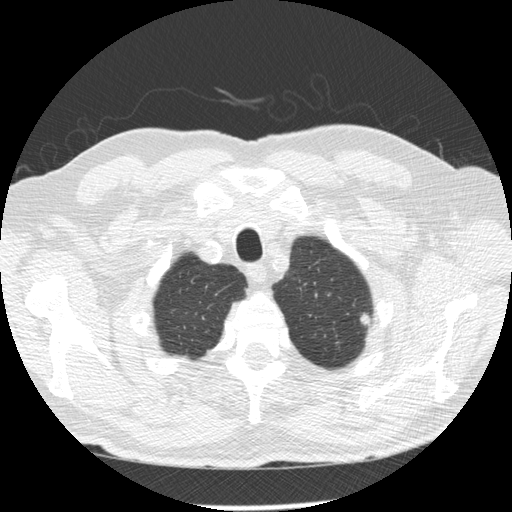
Axial slice from a low-dose chest CT screening exam; third annual screen; lung window (W 1500 / L -600 HU); 2.5 mm slice thickness; standard (soft-tissue) reconstruction kernel (STANDARD); 512 × 512 image matrix. Male, age 73 years at enrolment. Former smoker at enrolment.
Lesion marked by an expert reader, bounding box [x1, y1, x2, y2] px = [350, 298, 389, 337]. The exam's reader record, not a measurement of the box and not confirmed to be the same lesion: non-calcified nodule or mass ≥4 mm, left upper lobe, 8 × 7 mm, poorly defined margins, mixed attenuation, pre-existing on the prior screen: no. Later outcome: lung cancer diagnosed 93 days after this screen — adenocarcinoma, NOS, left upper lobe, poorly differentiated (G3), stage IB (AJCC 6th edition), 10 mm at pathology.